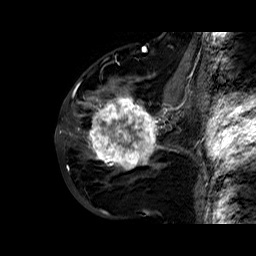
Breast MRI (dynamic contrast-enhanced), one sagittal slice. Slice 28 of 60 in the series (ordered by position). Dynamic contrast-enhanced series, time point 2 of 6 at this slice position (early post-contrast). 1.5 T. TE 6.4 ms, TR 32.8 ms. 4 mm slice thickness. 256 × 256 image matrix. Female patient. From the clinical record (not read from this slice): setting: breast cancer imaged before/during neoadjuvant chemotherapy; receptor status: HR-positive, HER2-negative.
Outlined on this slice (semi-automatic segmentation, software-assisted and operator-edited):
- analysis volume of interest (the breast-tissue region the enhancement analysis was run in; not a lesion): bounding box <86,77,163,177> (left, top, right, bottom; pixels)
- tumour enhancement mask (voxels above the 100 % enhancement threshold inside the analysis volume of interest): <86,87,163,170>